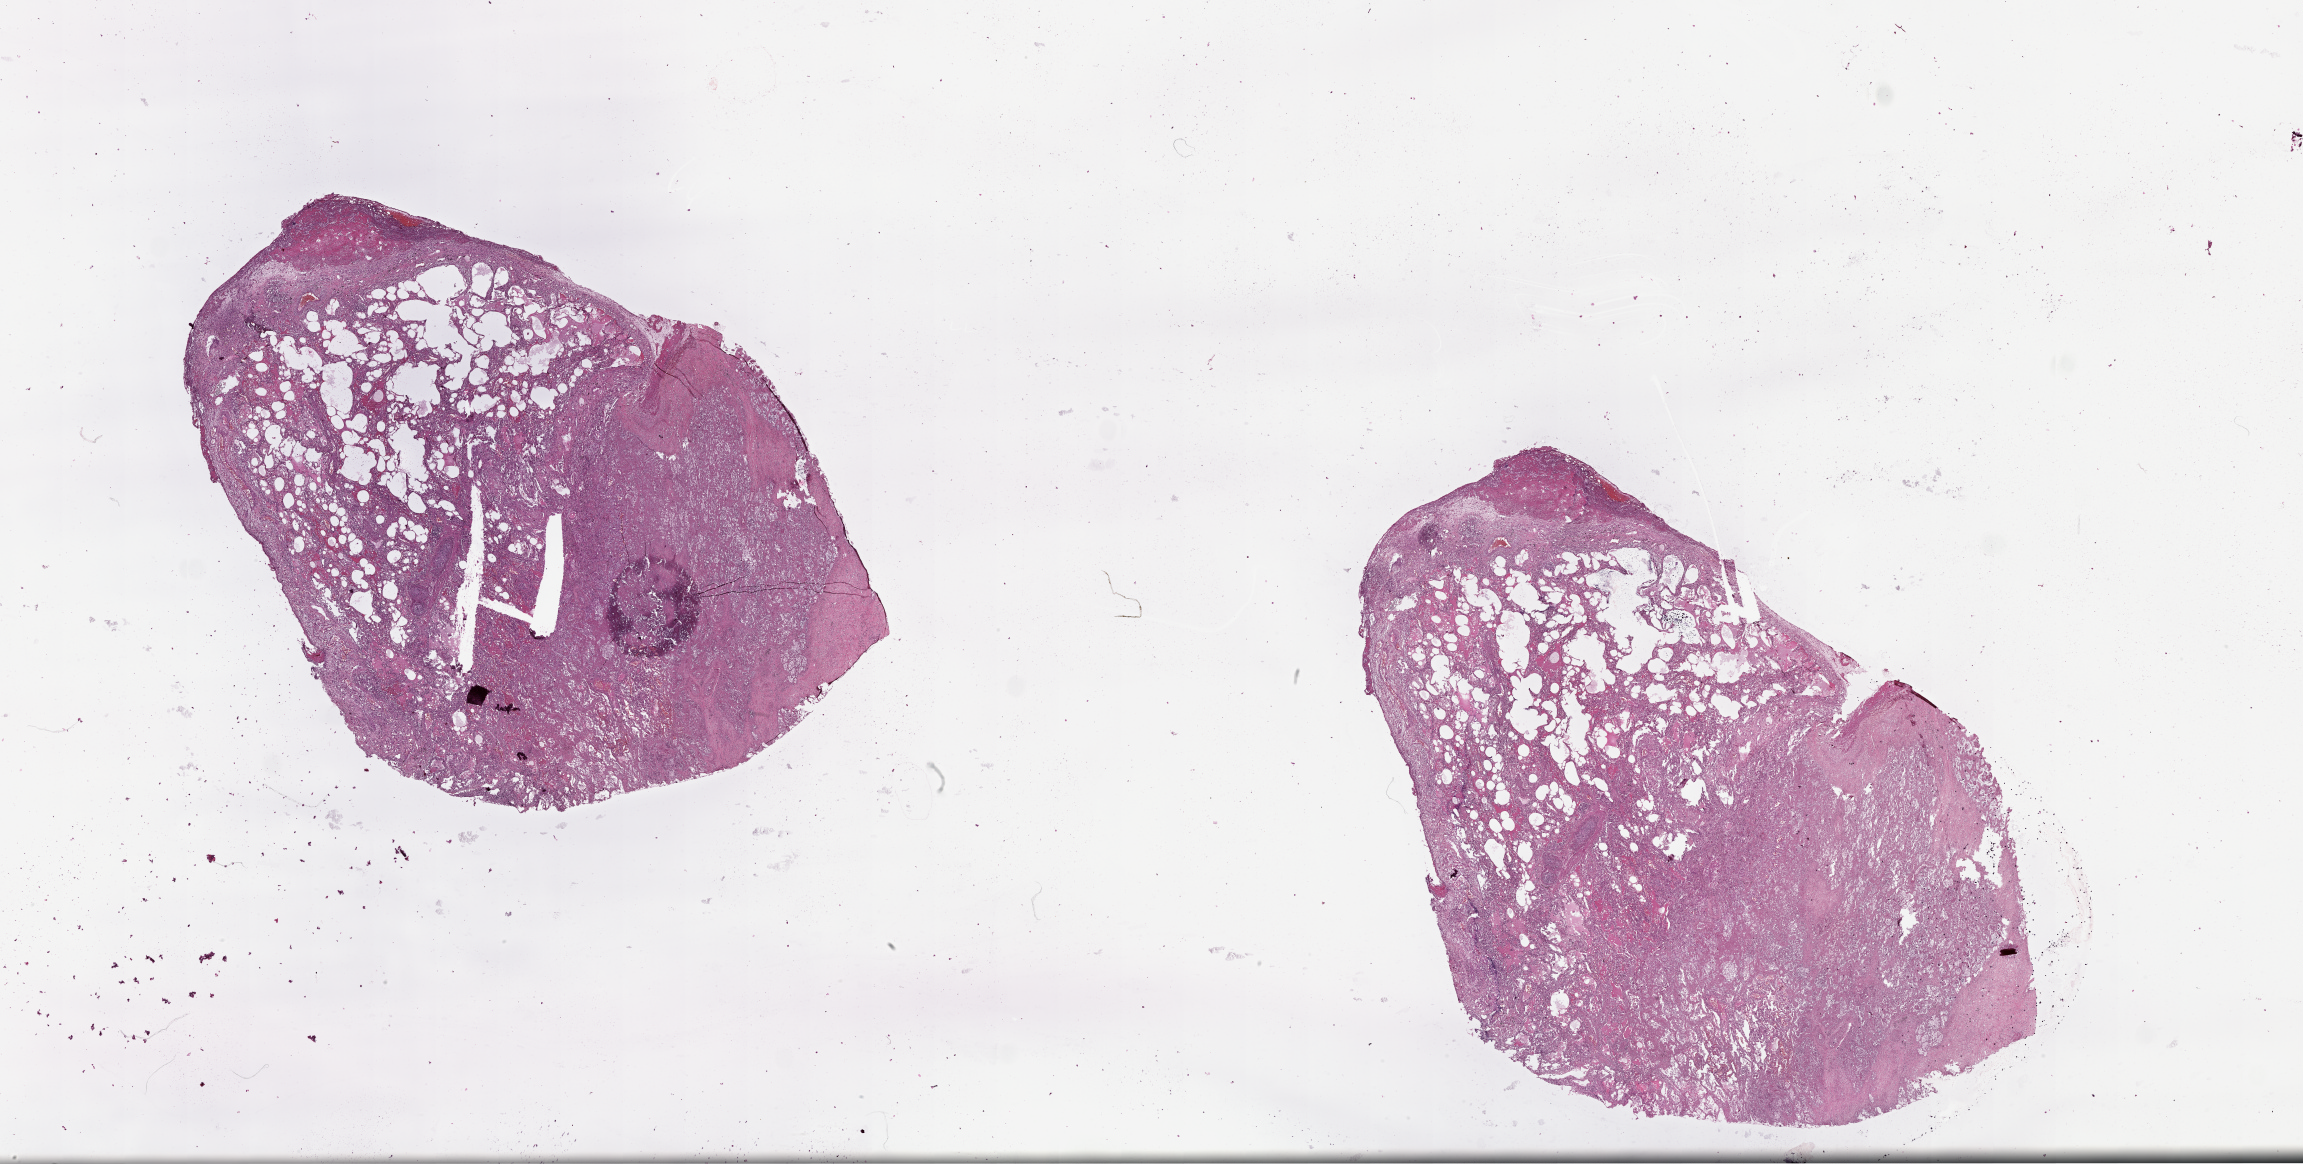
Whole-slide histology image, H&E — shown as a low-resolution overview of the whole scanned area (about 37.1 x 18.7 mm, slide scanned at 20x). Normal (non-tumour) tissue sample, lung. Patient: male, age 68 years.
This section: normal (non-tumour) tissue from the same patient. Patient diagnosis (cohort enrolment): squamous cell carcinoma (lung).